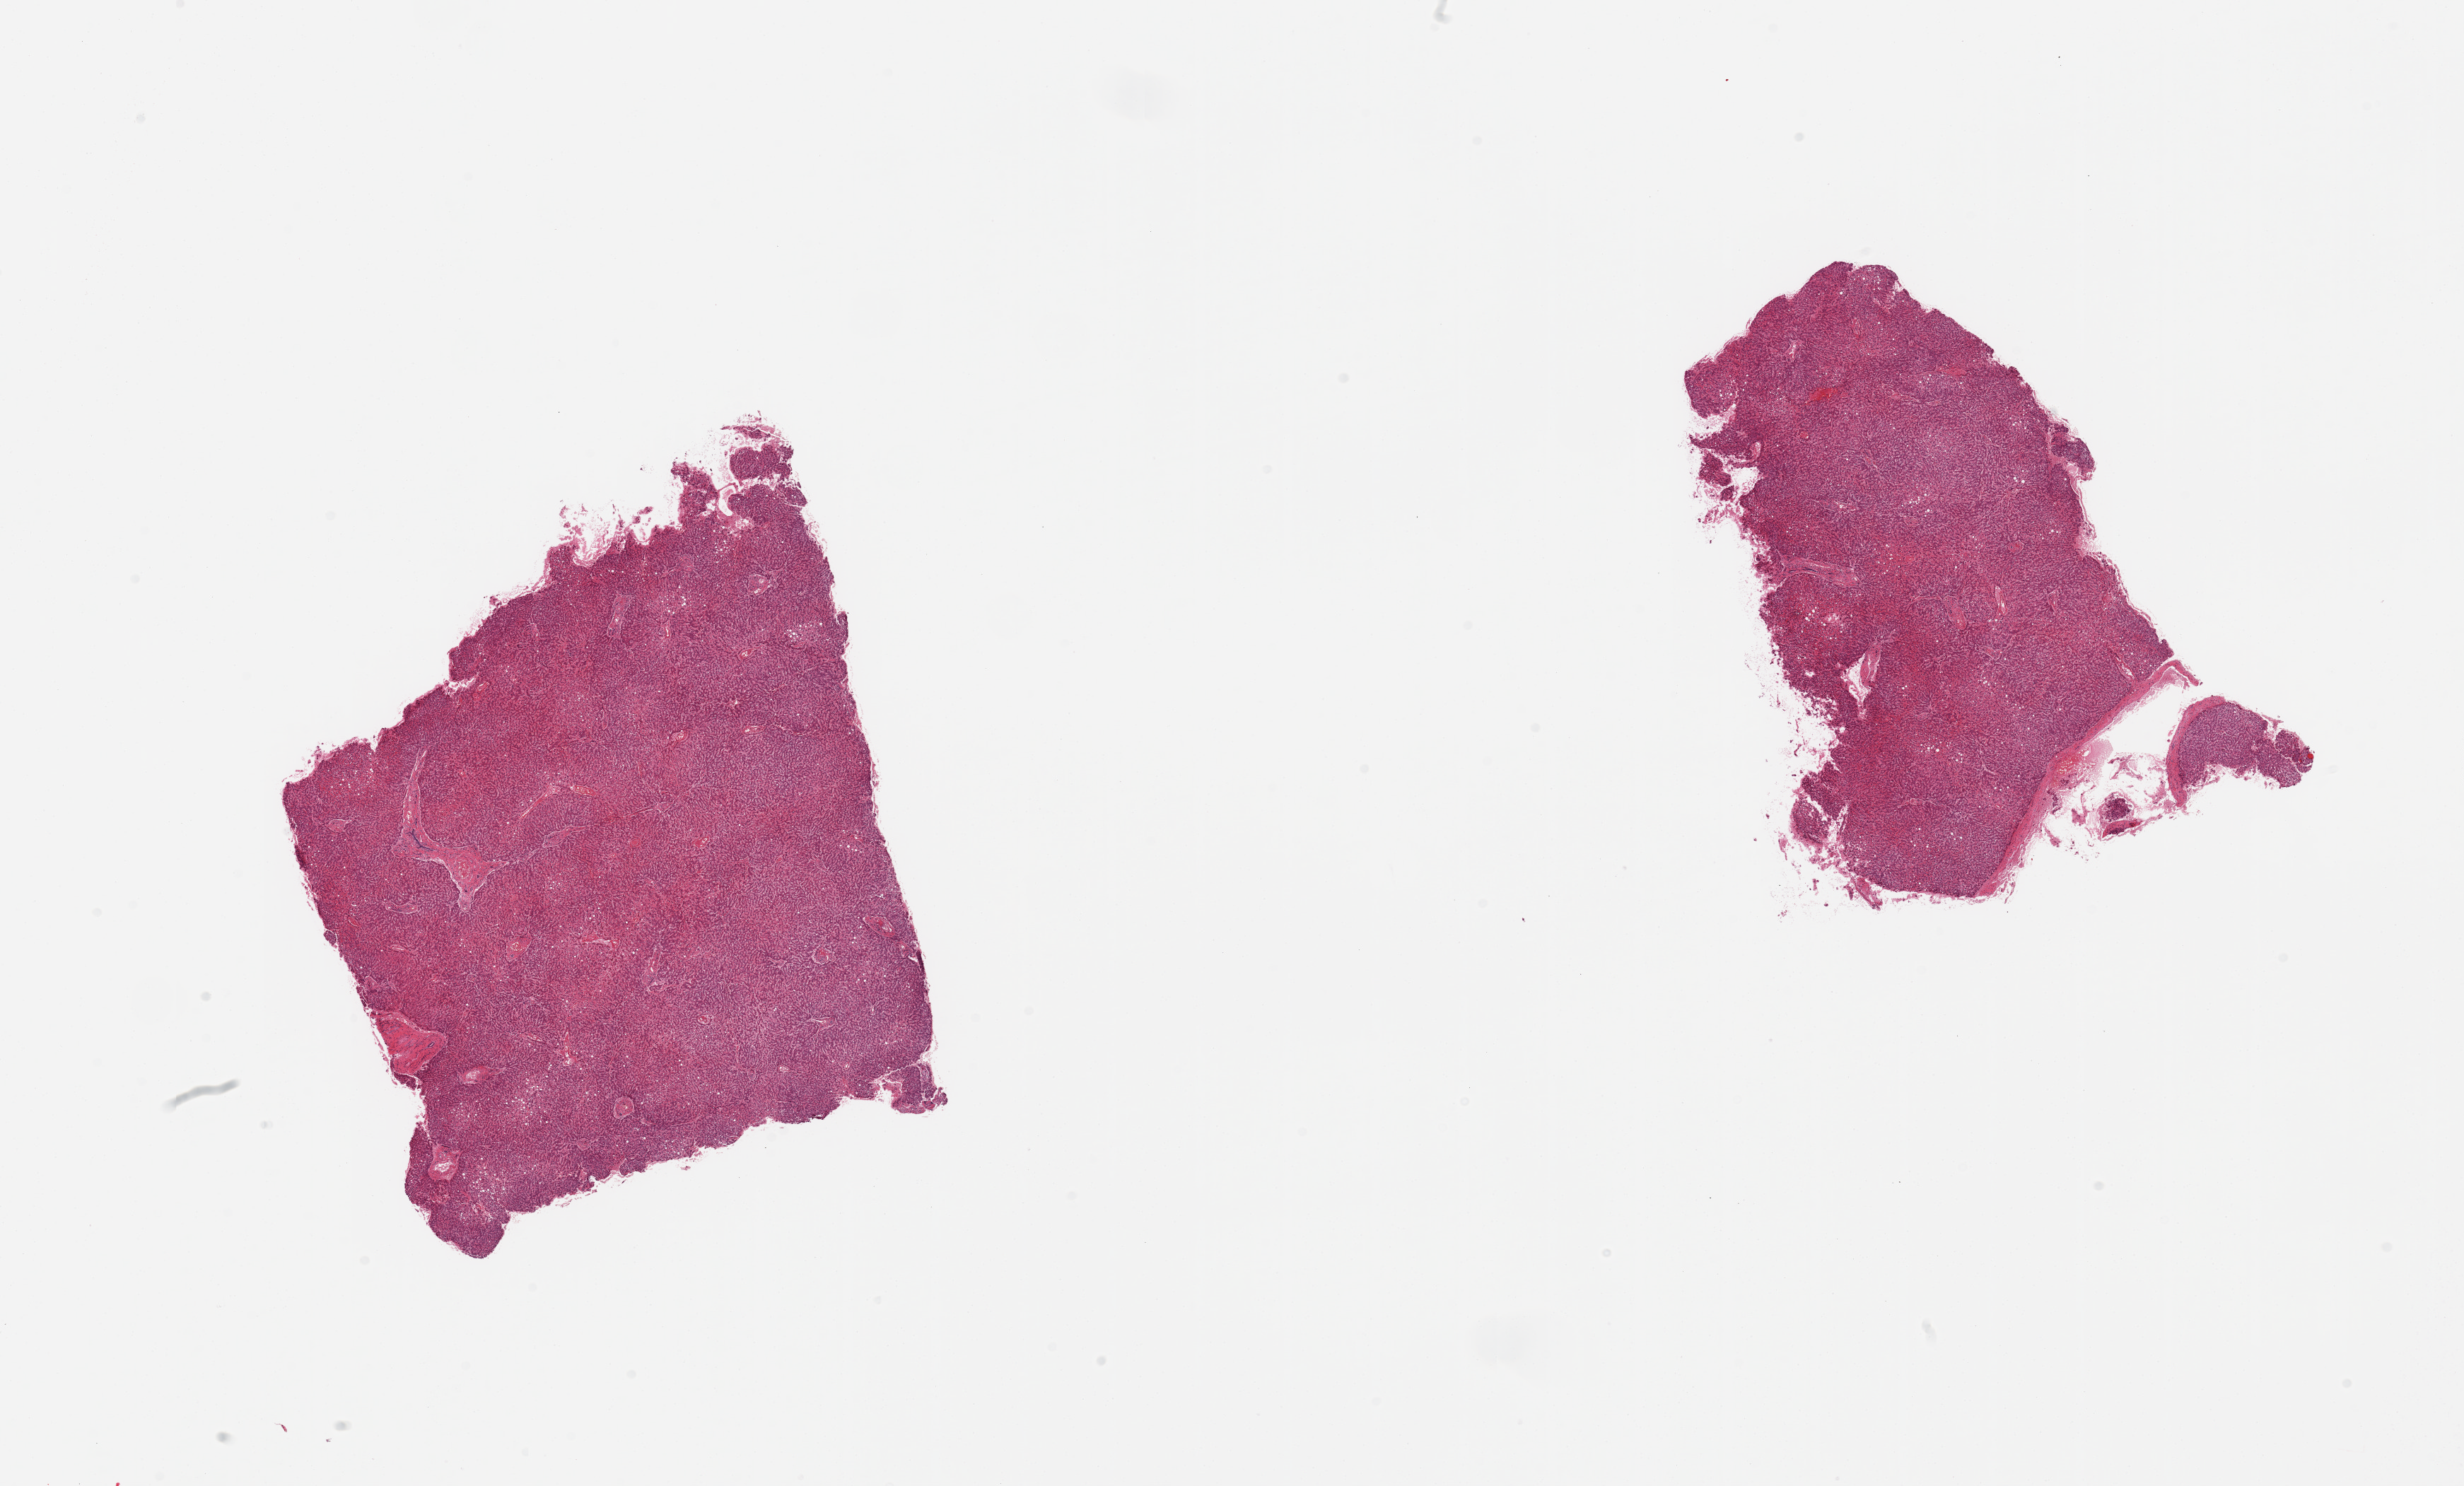
Digitized hematoxylin and eosin (H&E)-stained section, shown as a low-resolution overview of the whole scanned area (about 27.6 x 16.6 mm). PAXgene-fixed paraffin-embedded (PFPE) section. Section of liver (target tissue). Donor tissue sample.
* pathologist's review note for this sample: 2 pieces, micro (mainly) and macrovesicular steatosis involves ~70% parenchyma